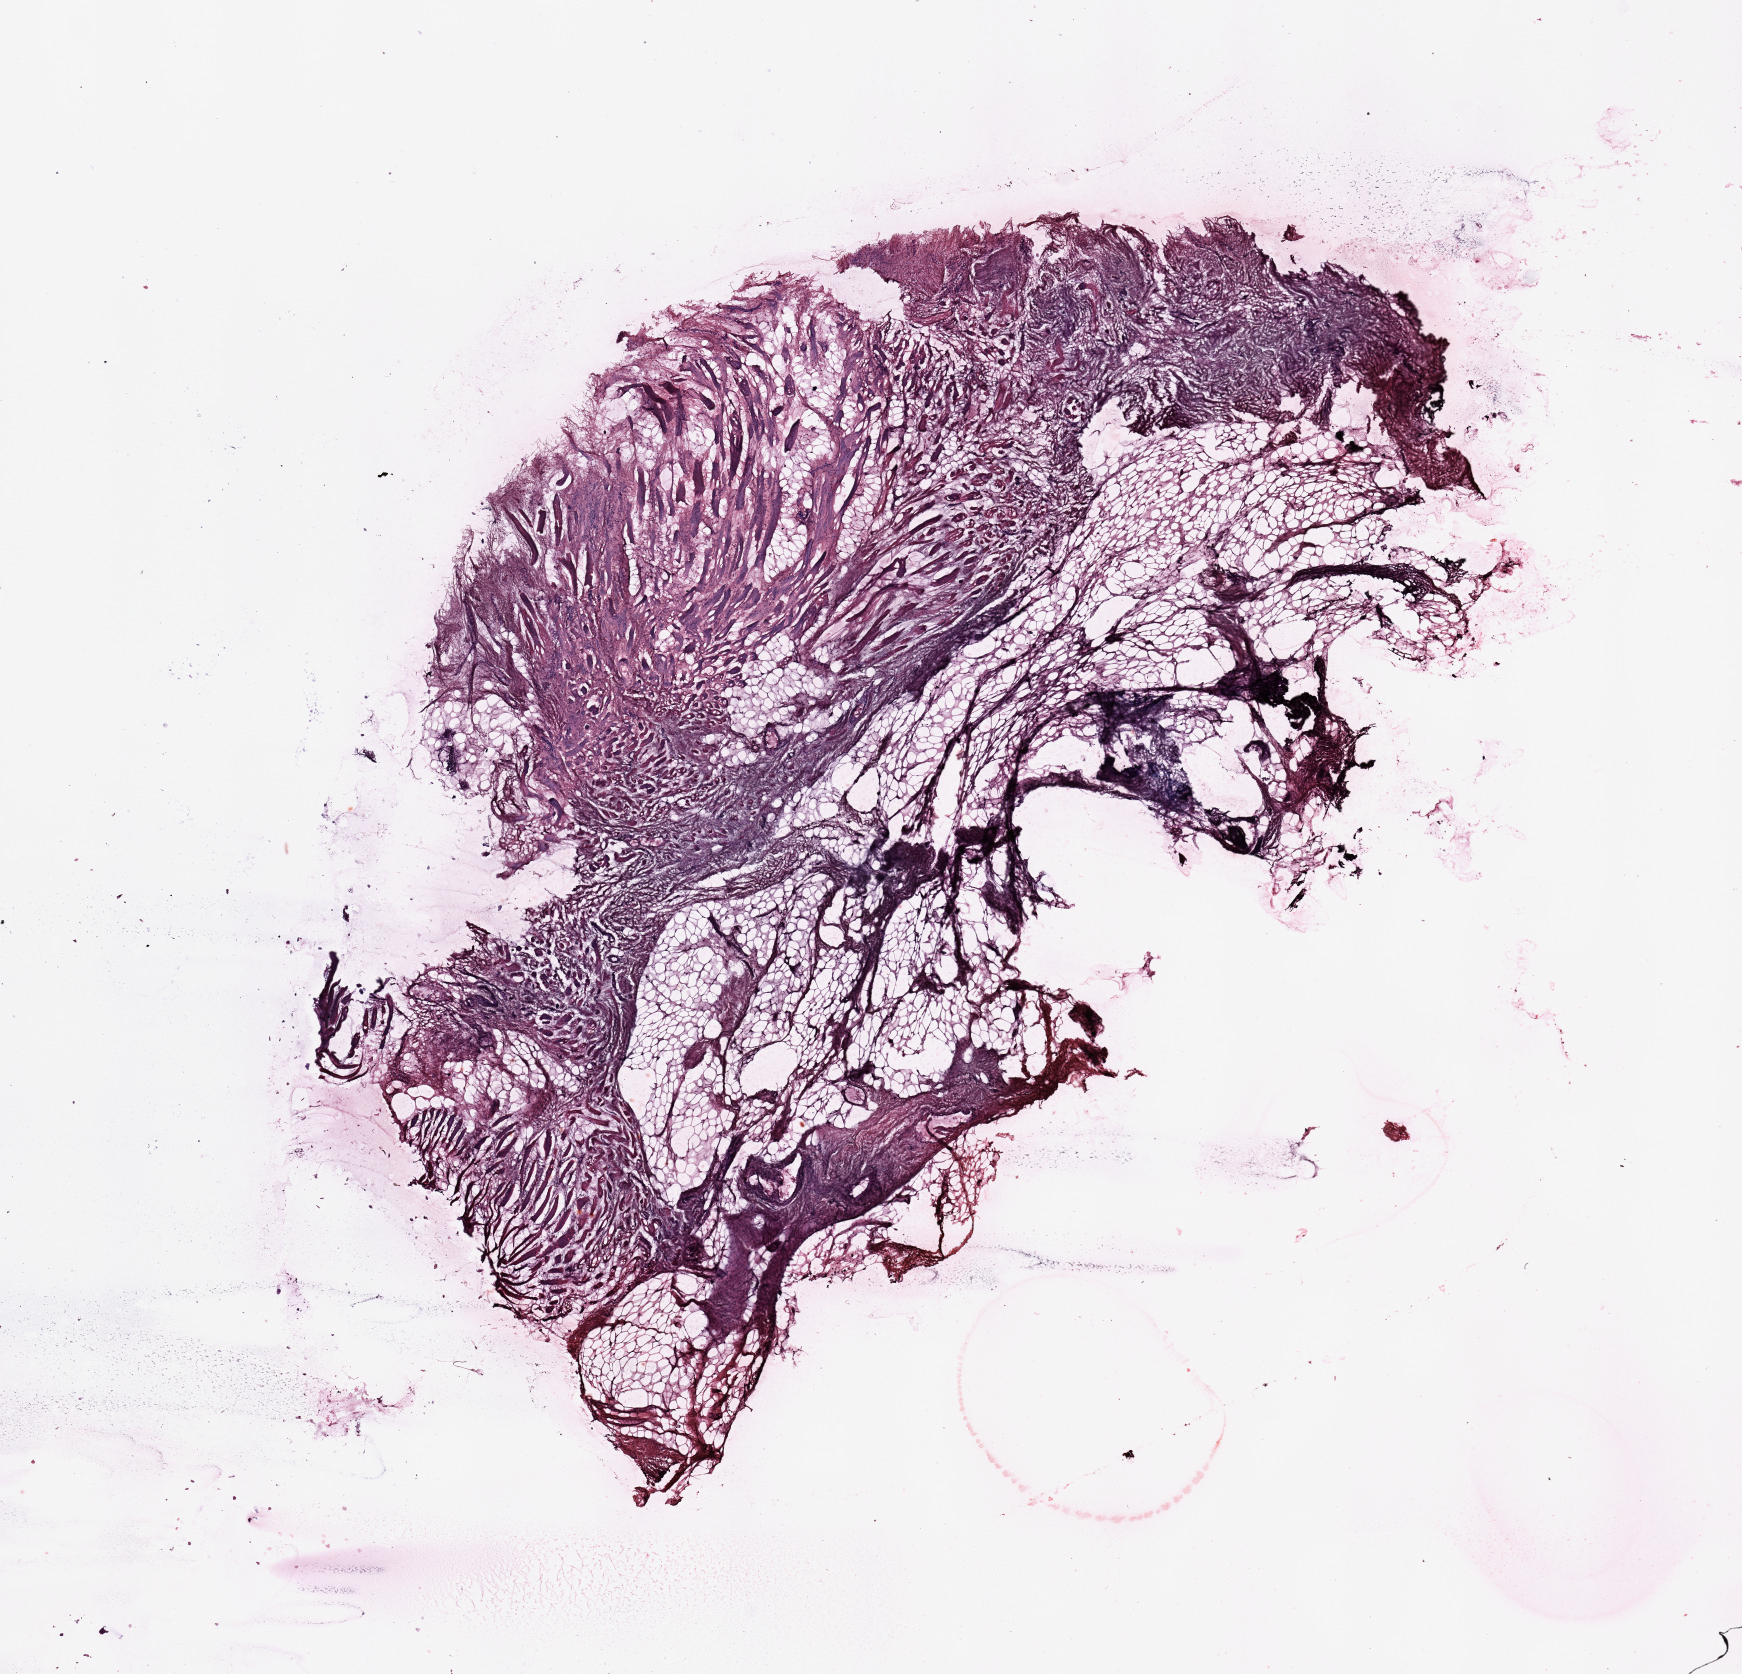
Digitized H&E-stained tissue section (whole slide), shown as a low-resolution overview of the whole scanned area (about 13.8 x 13.2 mm), normal (non-tumour) tissue sample. Patient: female, age 42 years.
This section: normal (non-tumour) tissue from the same patient. Patient diagnosis (cohort enrolment): sarcoma (site not recorded at cohort level).